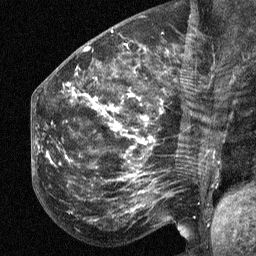
Breast MRI (dynamic contrast-enhanced), one sagittal slice. Position 25 of 64 along the scan axis. Dynamic contrast-enhanced study with each time point stored as its own series, time point 2 of 3 at this slice position (early post-contrast, ordered by acquisition time). 1.5 T. TE 4.8 ms, TR 27 ms. 2.3 mm slice thickness. 256 × 256 image matrix. Female patient, age 50 years. From the clinical record (not read from this slice): setting: breast cancer imaged before/during neoadjuvant chemotherapy; receptor status: HER2-positive.
Outlined on this slice (semi-automatic segmentation, software-assisted and operator-edited):
- analysis volume of interest (the breast-tissue region the enhancement analysis was run in; not a lesion): bounding box <53,64,211,218> (left, top, right, bottom; pixels)
- tumour enhancement mask (voxels above the 90 % enhancement threshold inside the analysis volume of interest): <75,96,151,176>